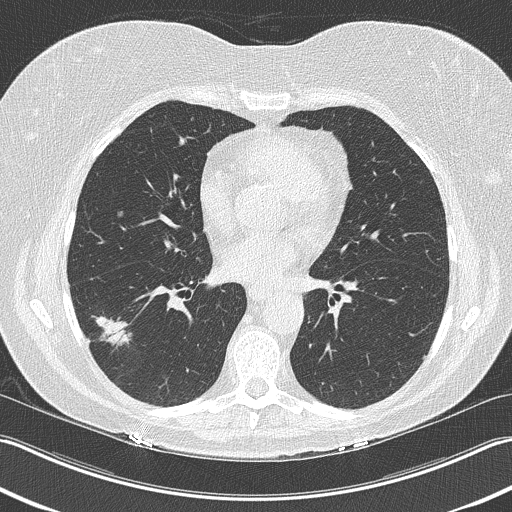
Low-dose screening chest CT, one axial slice. Slice 109 of 210 in the series (ordered by position). 120 kVp. Lung window (W 1500 / L -600 HU). 2 mm slice thickness. 512 × 512 image matrix, field of view 348 × 348 mm.
Structures marked on this image (expert manual segmentation):
- lesion 1 (tumor, lower lobe of right lung): box from (x=95, y=316) to (x=132, y=349) px